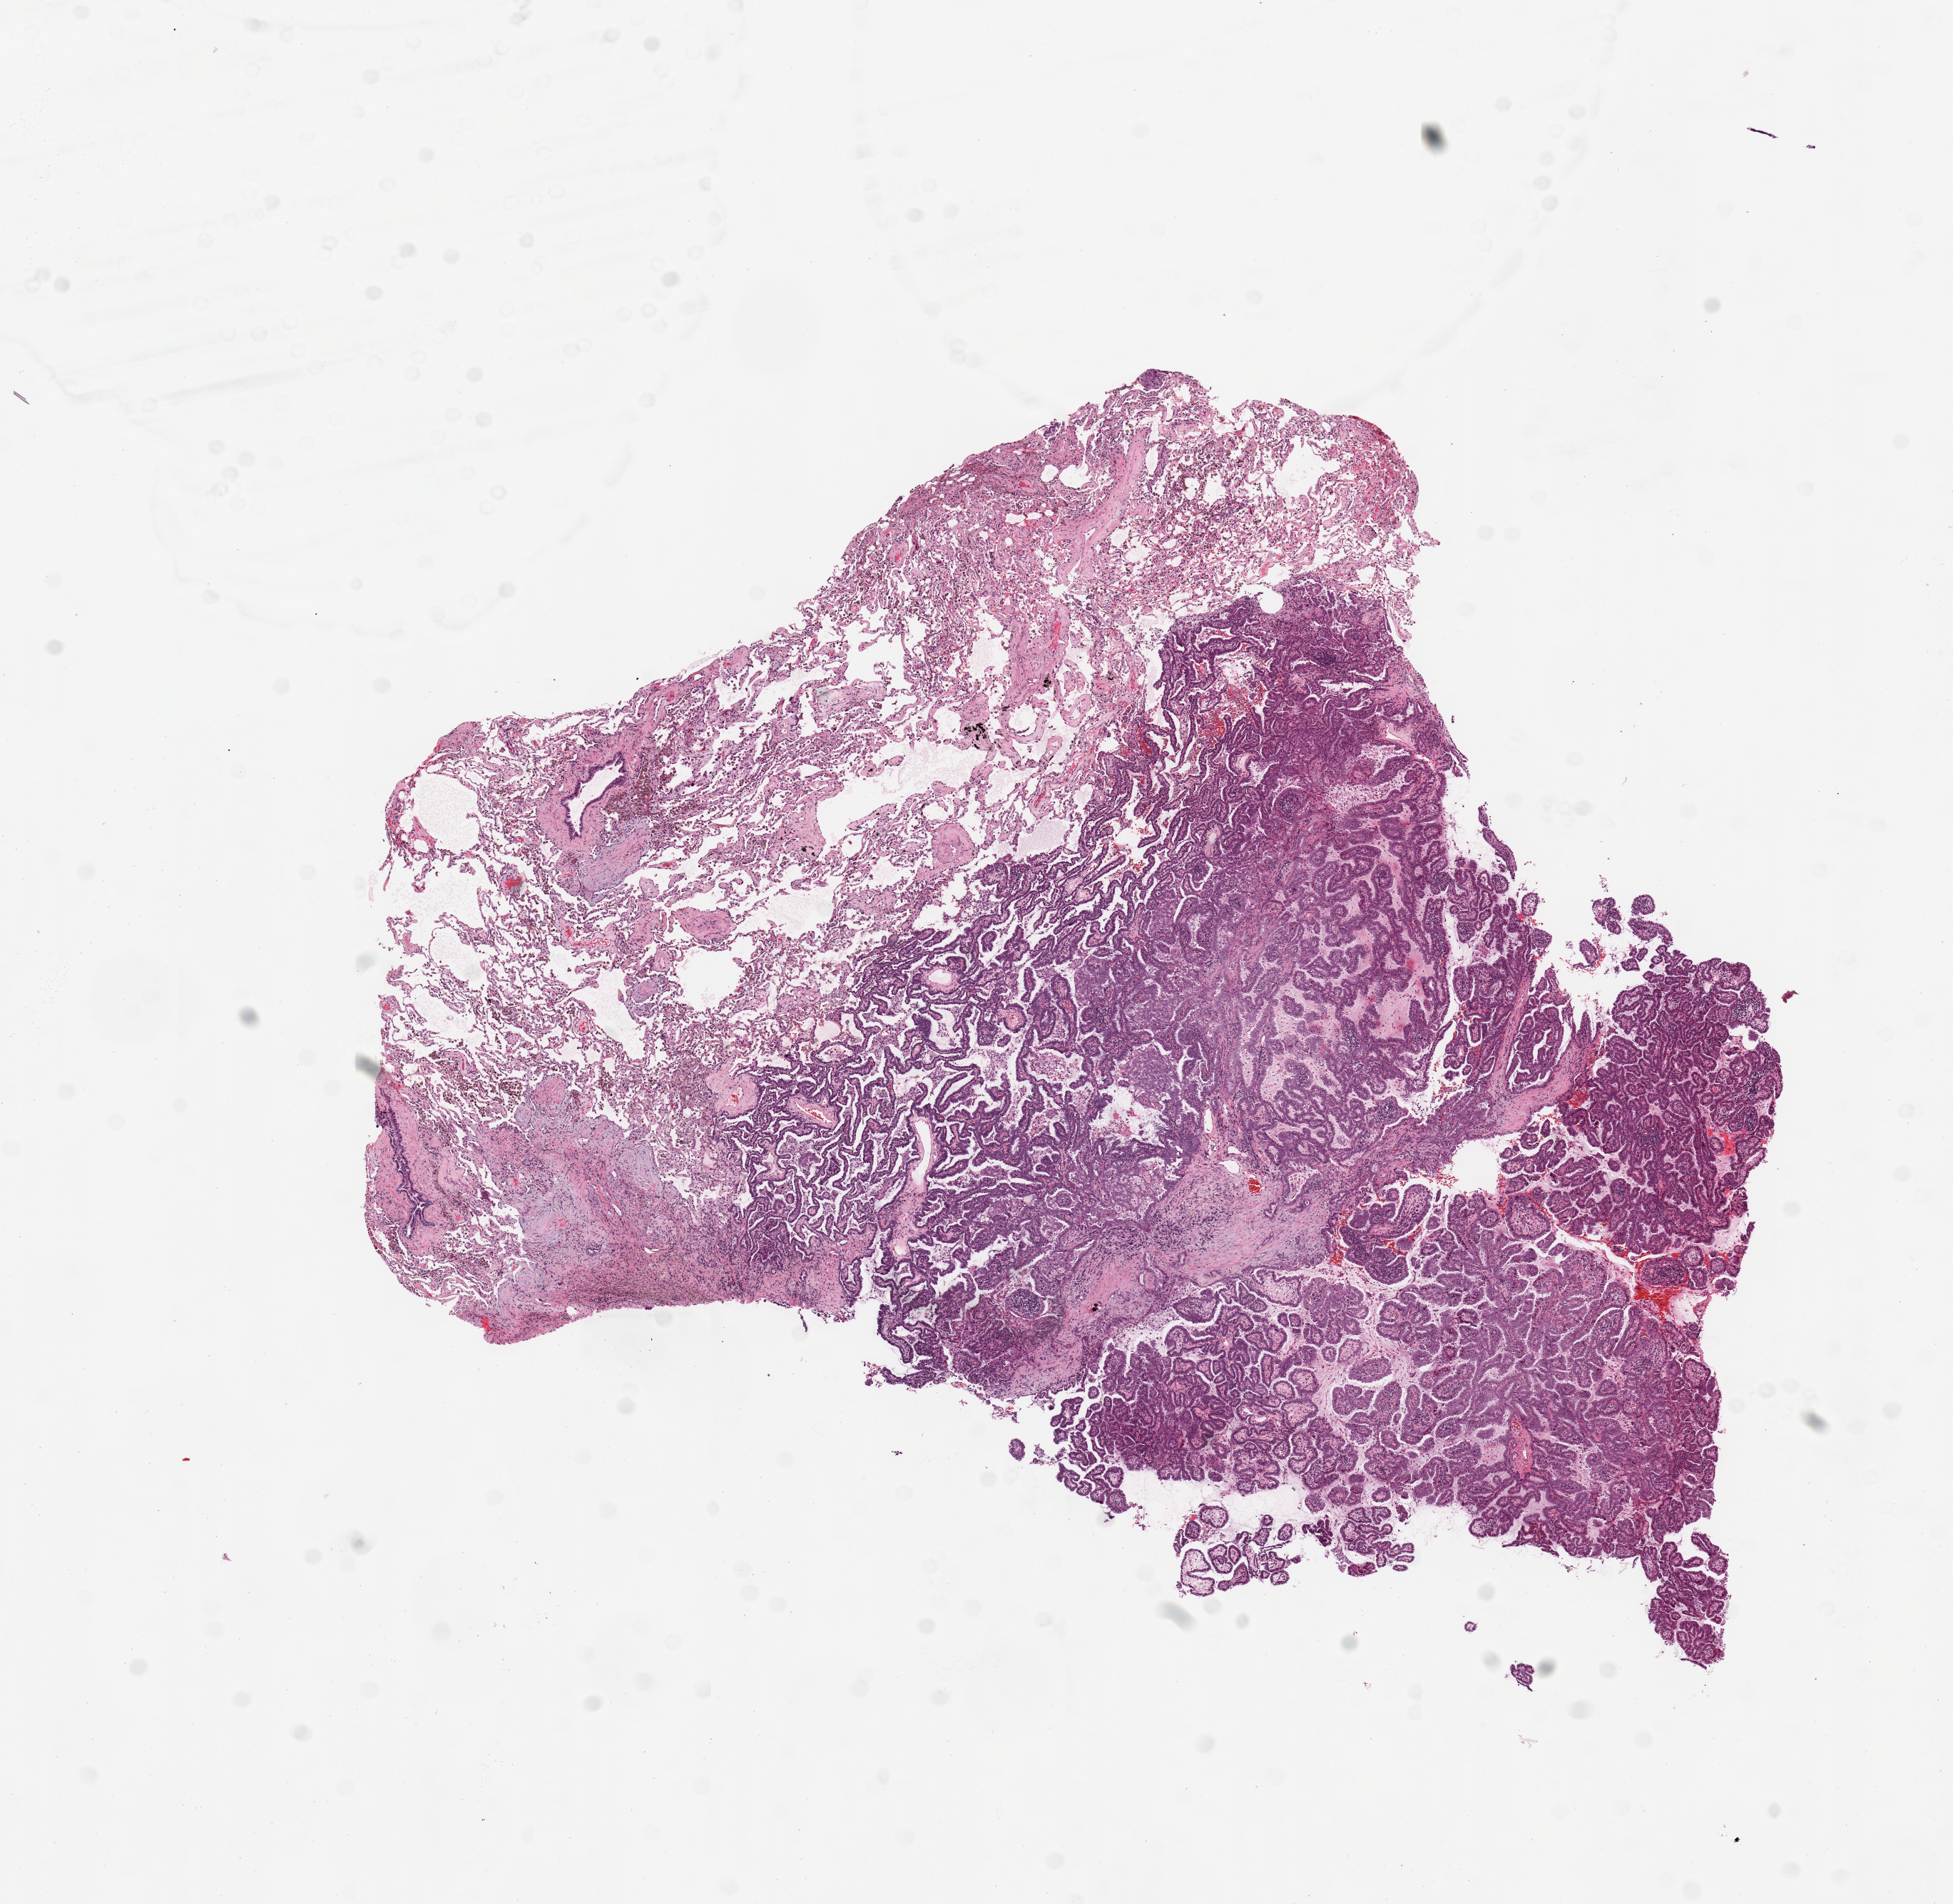
H&E whole-slide image, a low-resolution overview of the entire scanned area, about 10.8 x 10.6 mm (acquisition: 20x scan), lung, tumour tissue. Patient: male, age 70 years. Histologic grade: G1 (well differentiated).
* primary tumour site (as recorded): right upper lobe
* diagnosis: Adenocarcinoma, NOS
* AJCC pathologic stage: IA